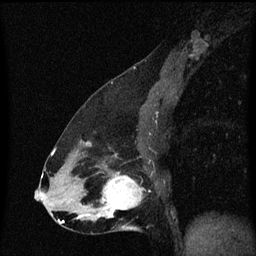
Breast MRI (dynamic contrast-enhanced), one sagittal slice; position 32 of 60 along the scan axis; dynamic contrast-enhanced series, image 2 of 3 at this slice position (ordered by acquisition); 1.5 T; TE 4.2 ms, TR 8.4 ms; 256 × 256 image matrix. Female patient, age 47 years.
Annotated regions visible in this slice (semi-automatic segmentation, software-assisted and operator-edited):
- analysis volume of interest (the breast-tissue region the enhancement analysis was run in; not a lesion): bounding box (x1, y1, x2, y2) in pixels: (100, 172, 143, 219)
- tumour enhancement mask (voxels above the 70 % enhancement threshold inside the analysis volume of interest): (102, 174, 143, 217)